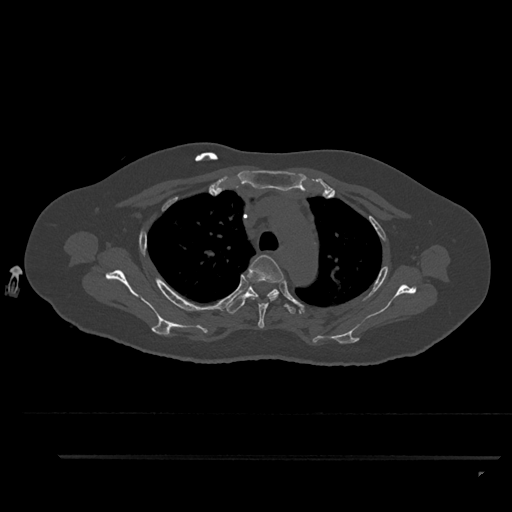
CT including the spine, one axial slice. Position 664 of 797 along the scan axis. Bone window (W 1800 / L 400 HU). 0.5 mm slice thickness. 512 × 512 image matrix, field of view 408 × 408 mm. Patient: female, 44 years. Case-level facts recorded for this patient, not image findings: primary cancer: renal; vertebrae with lytic lesions (as recorded): L1.
Annotated regions visible in this slice (semi-automatically segmented with operator editing):
- T3 vertebra: box from (x=246, y=255) to (x=284, y=328) px
- T4 vertebra: (x=227, y=286)–(x=296, y=314)